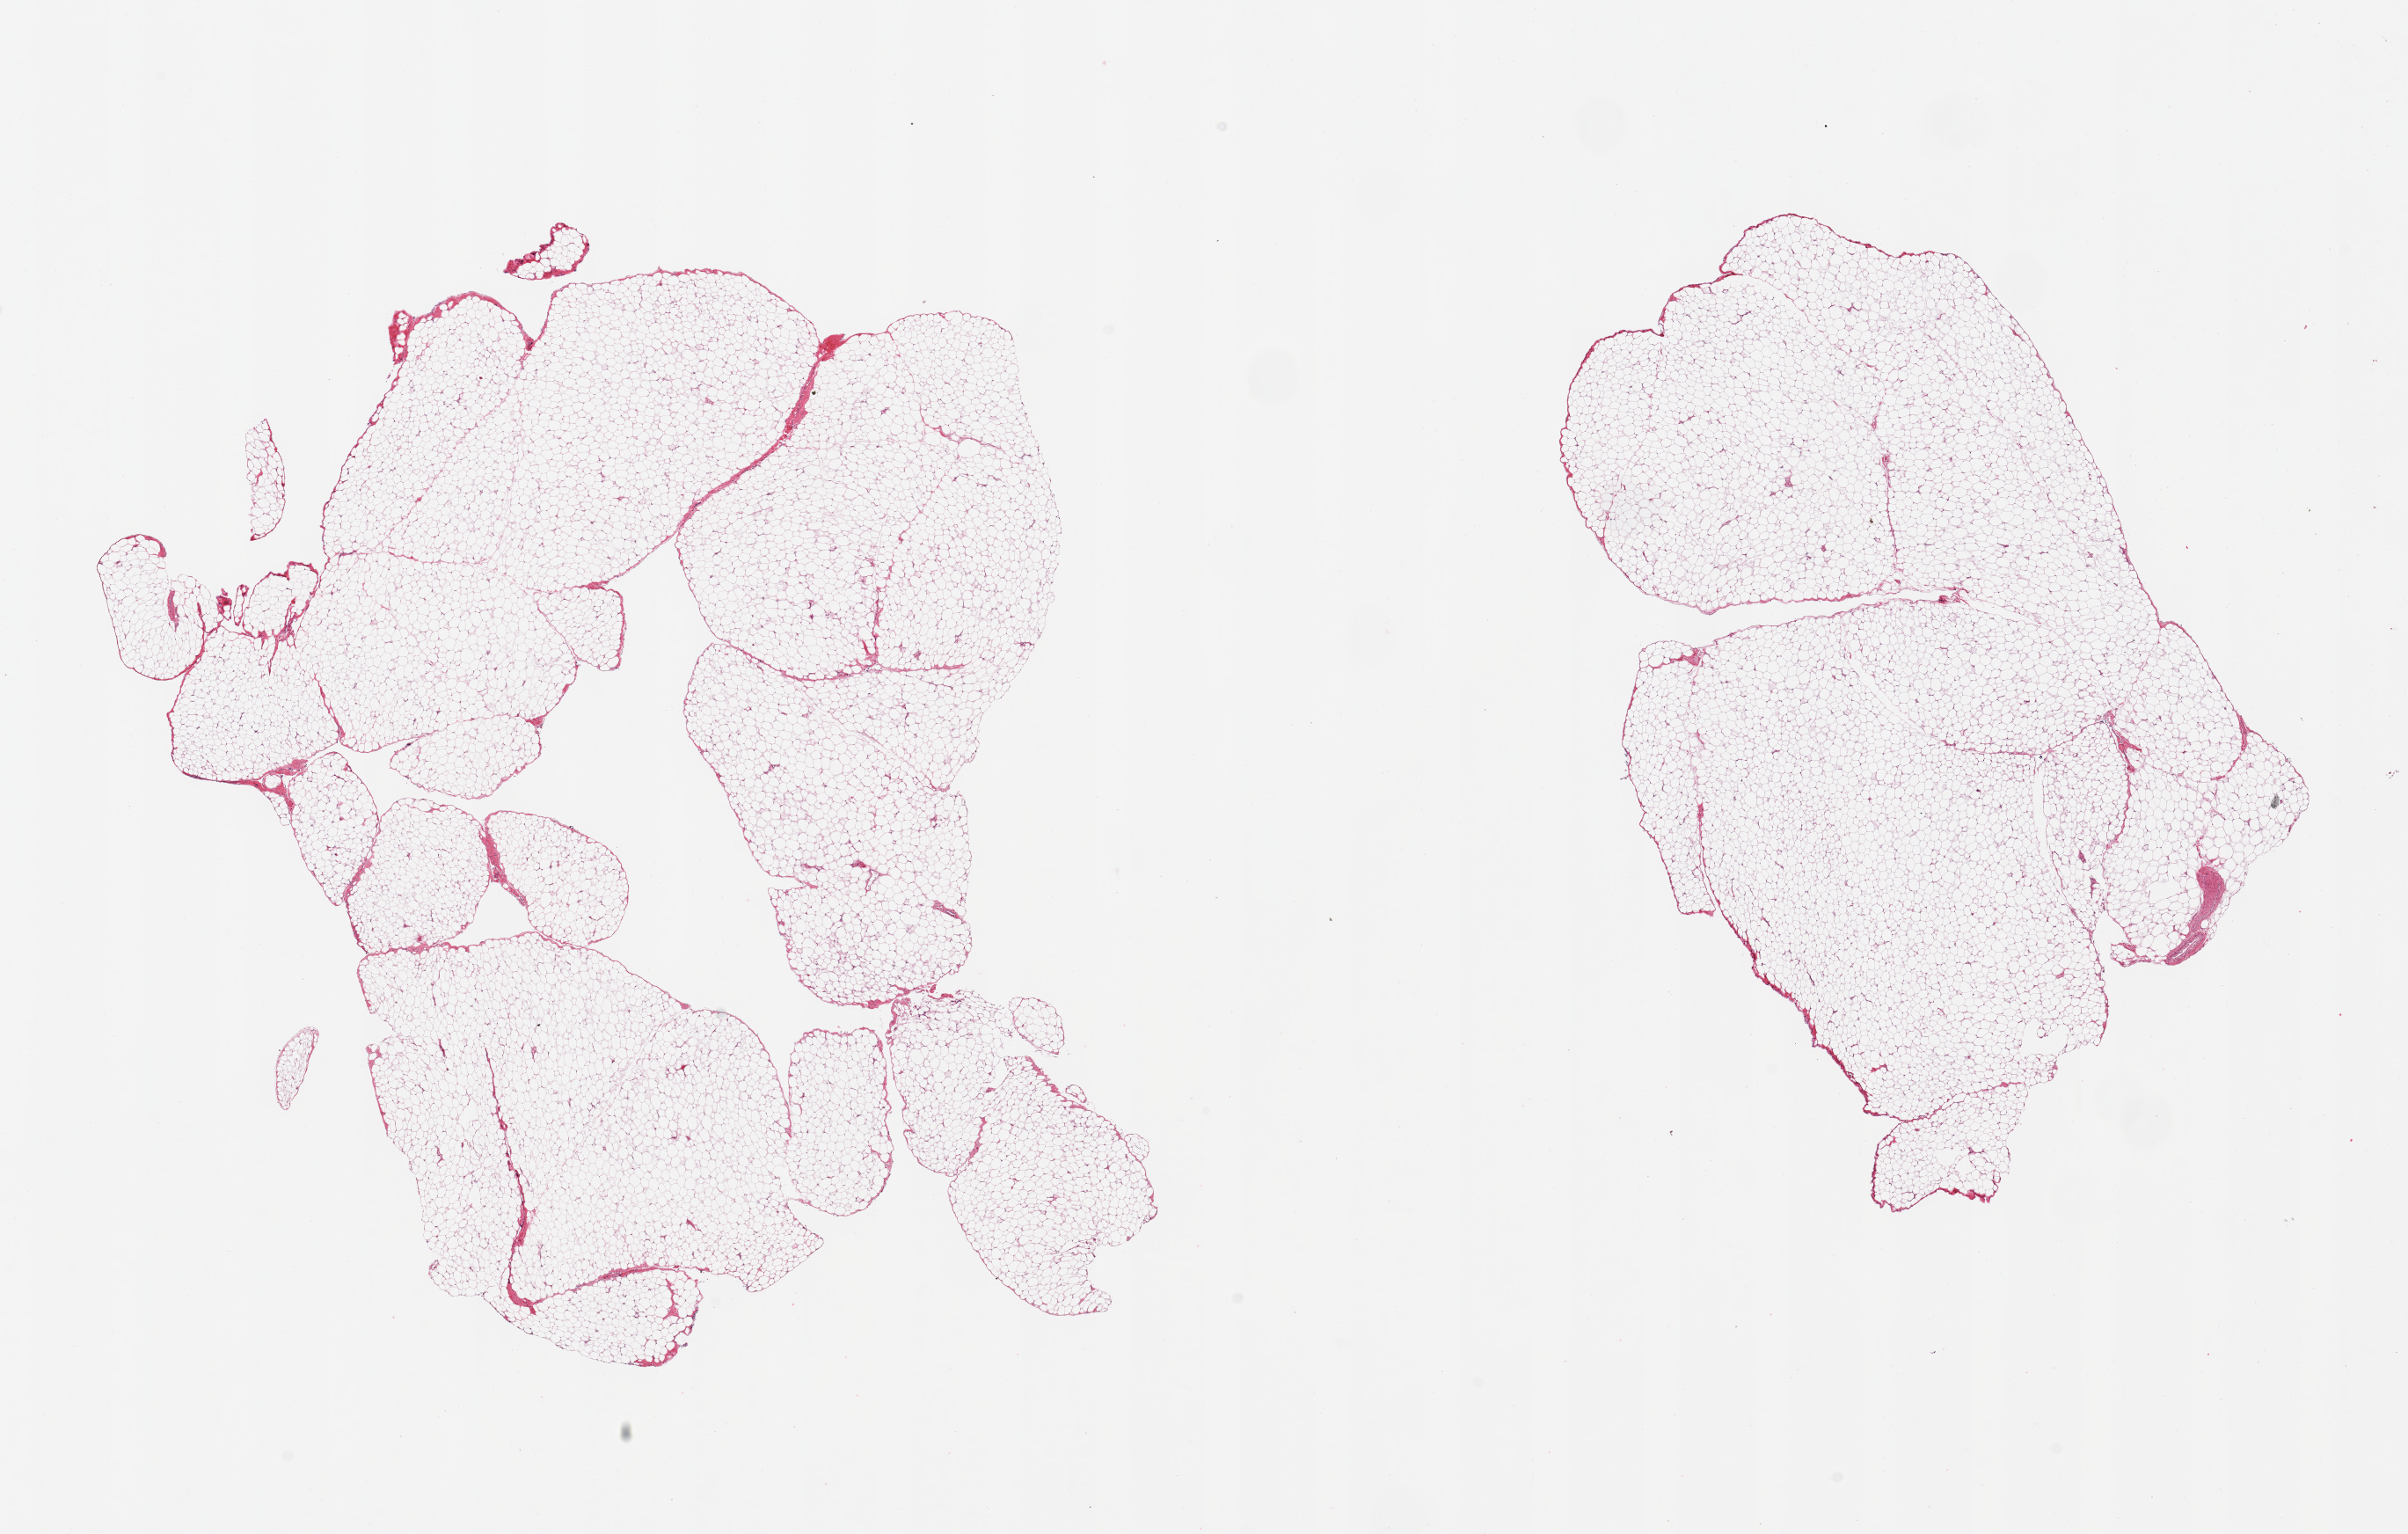
Haematoxylin and eosin whole-slide image, whole scanned area (about 21.7 x 13.8 mm, acquisition: 20x scan) shown as a low-resolution overview; PAXgene-fixed, paraffin-embedded tissue; target tissue: omentum; tissue donor sample. Female donor.
Reviewer comment on this tissue sample: 2 pieces; lobulated fat with minimal fibrous content.